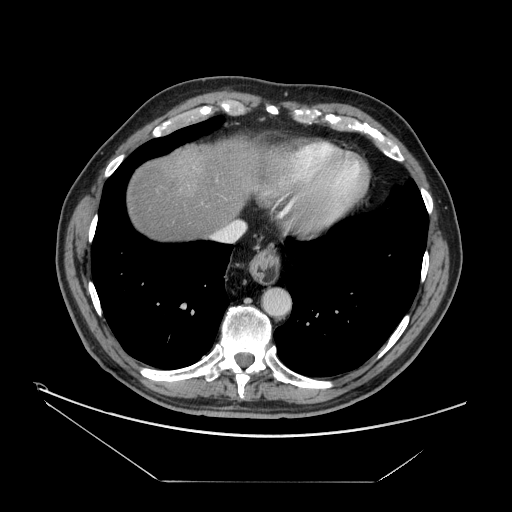
Contrast-enhanced abdominal CT, one axial slice; position 146 of 161 along the scan axis; reconstruction kernel STANDARD; 120 kVp; intravenous contrast given; soft-tissue window (W 400 / L 40 HU); 2.5 mm slice thickness; 512 × 512 image matrix, field of view 440 × 440 mm. Male patient, age 65 years. Case-level facts recorded for this patient, not image findings: diagnosis: colorectal cancer liver metastases, imaged before liver resection; multiple liver metastases: yes; largest metastasis: 4.2 cm.
Annotated regions visible in this slice (manually delineated by an expert):
- hepatic veins: bounding box (x1, y1, x2, y2) in pixels: (215, 221, 246, 242)
- liver: (126, 139, 254, 241)
- planned liver remnant (the part of the liver to remain after resection): (126, 138, 255, 240)